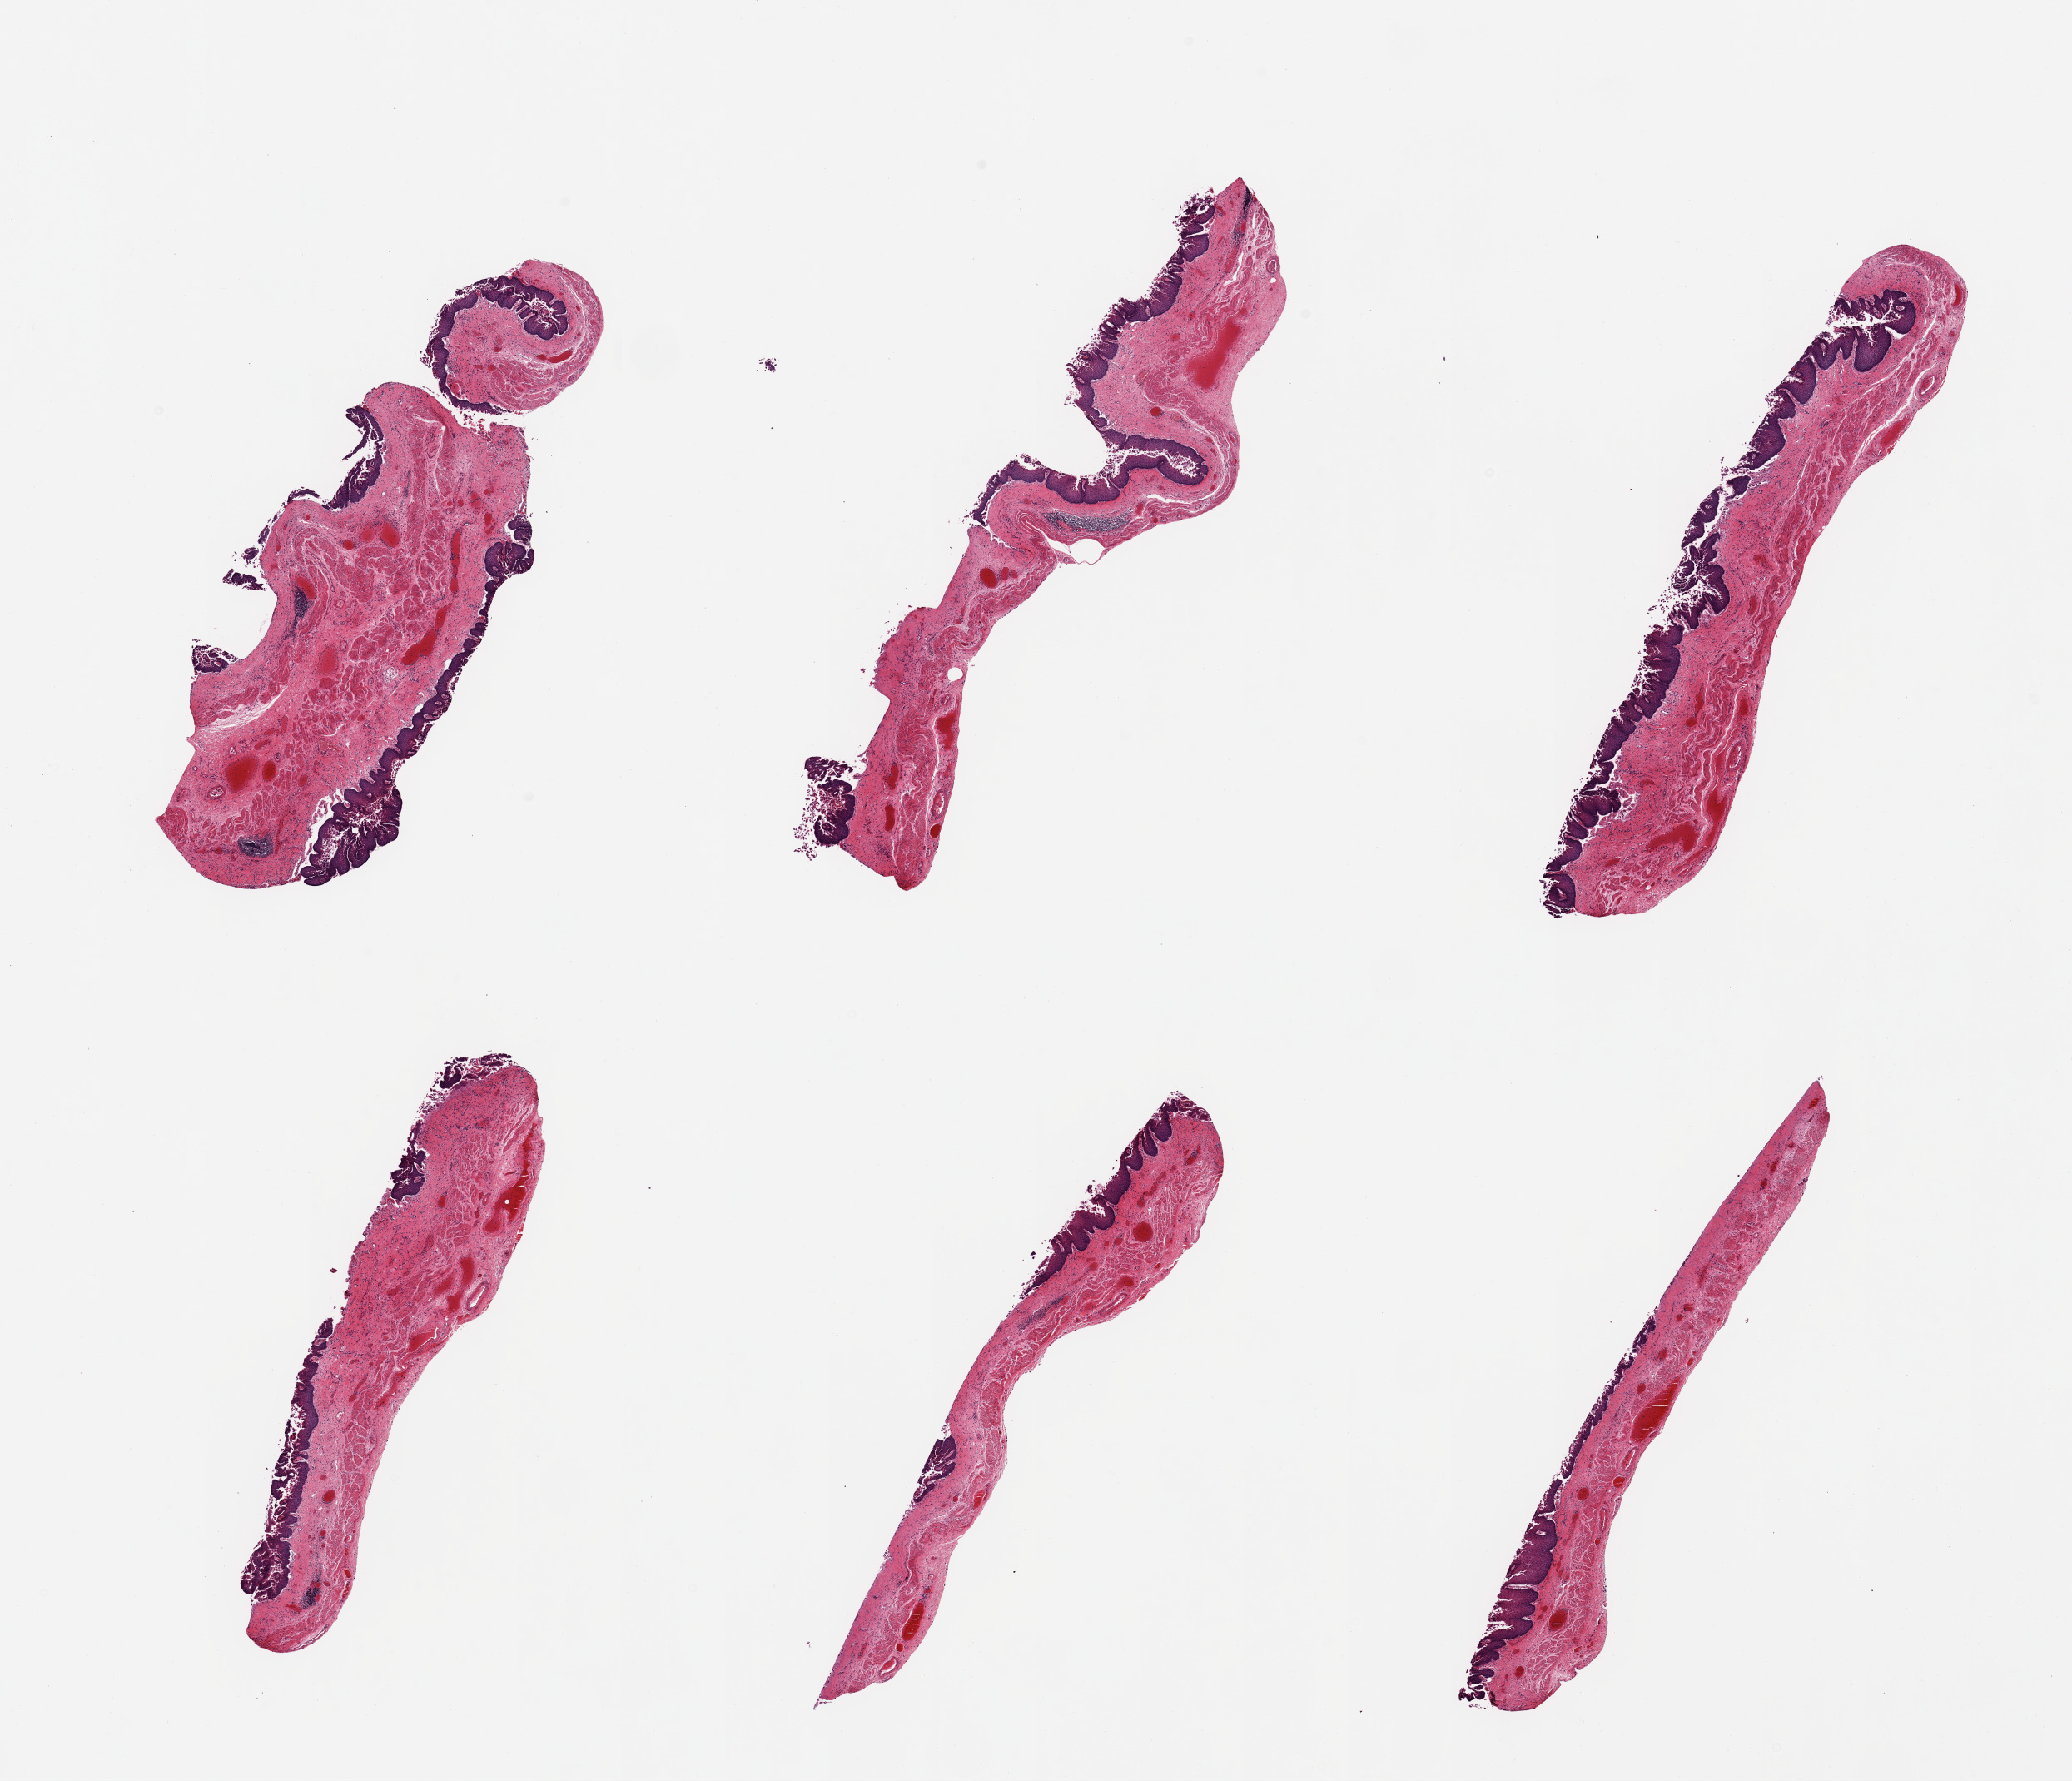
Whole-slide image, haematoxylin and eosin stain, brightfield — whole scanned area (about 19.7 x 16.9 mm) shown as a low-resolution overview. PAXgene-fixed, paraffin-embedded tissue. Section of esophageal mucous membrane (target tissue). Donor tissue sample. Donor: female.
Reviewer comment on this tissue sample: 6 pieces; mucosa partially autolyzed and sloughed; congestion.